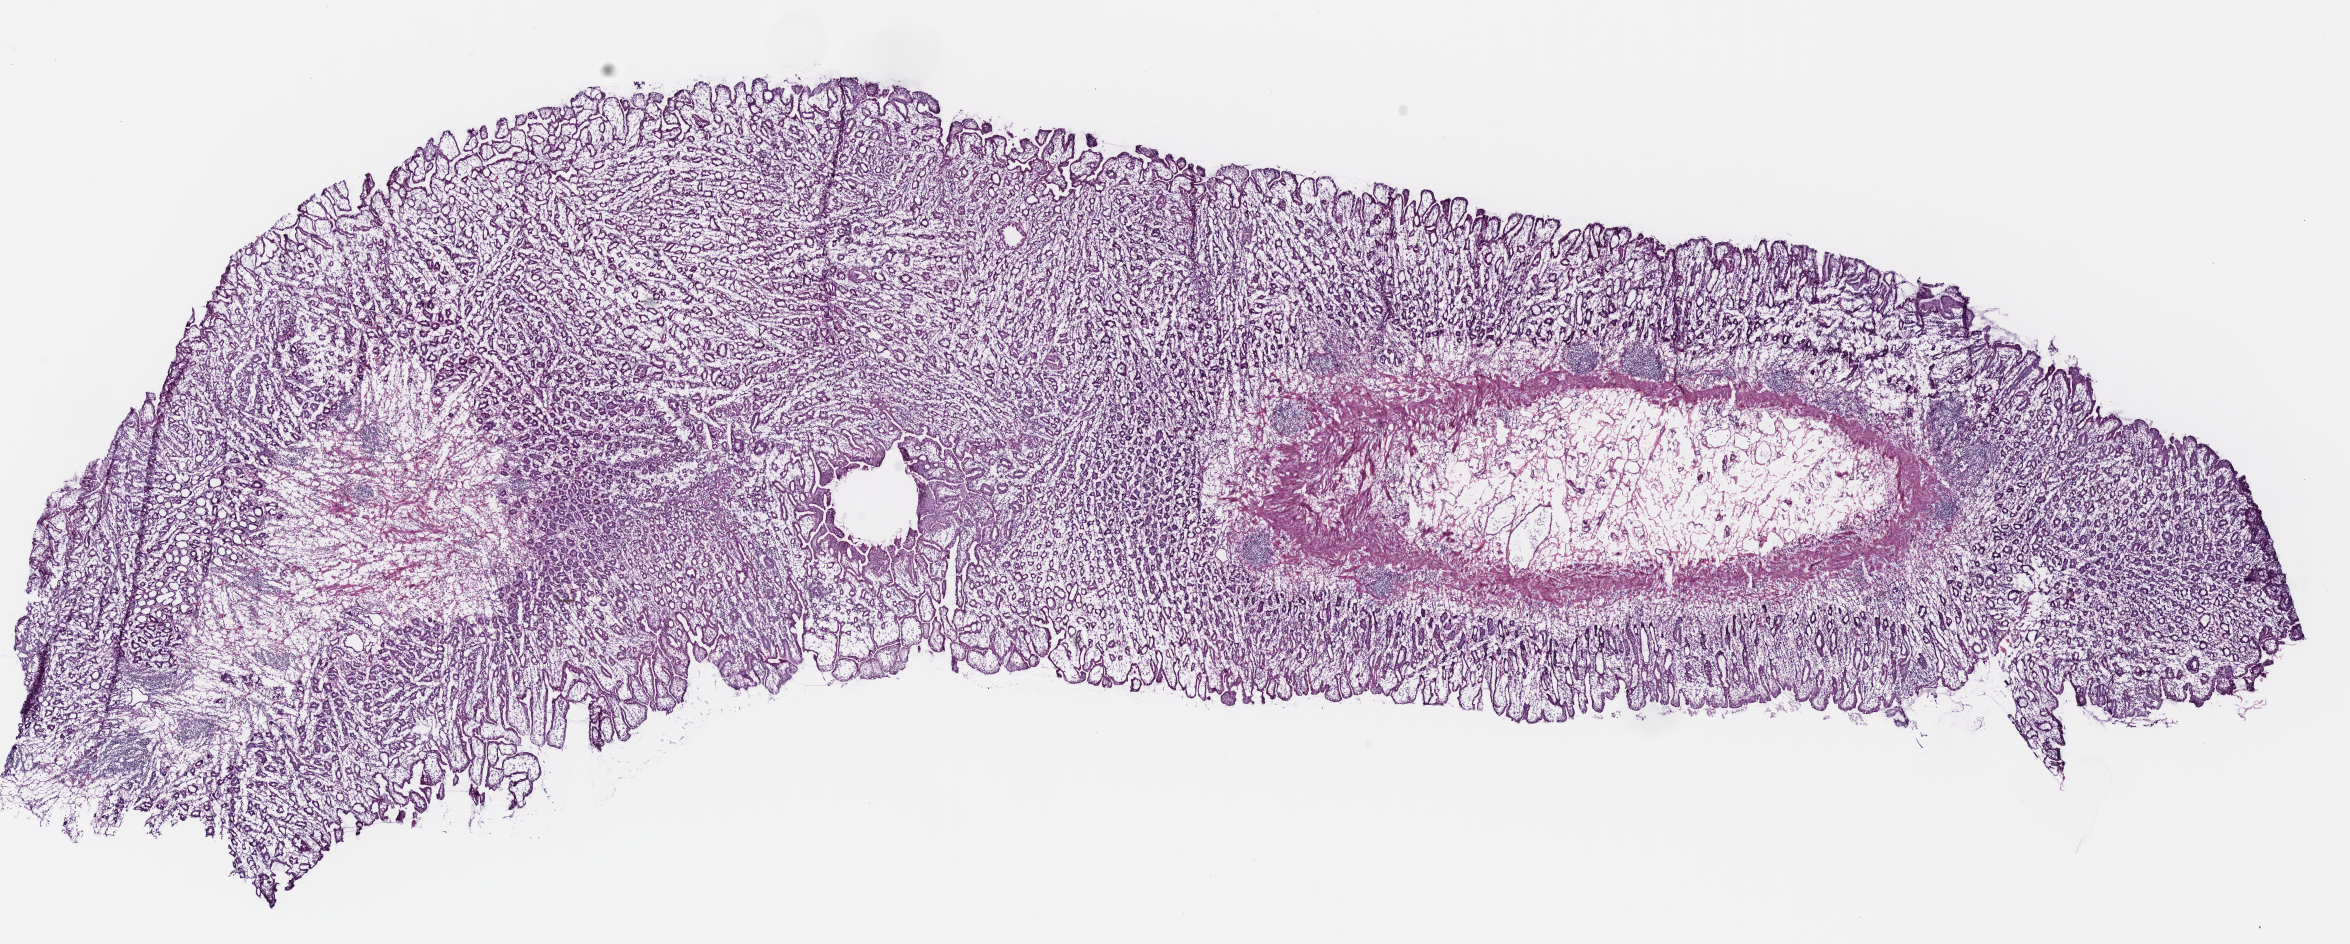
H&E whole-slide image — a low-resolution overview of the entire scanned area, about 18.5 x 7.4 mm (acquisition: 40x scan). Frozen section. Stomach, solid tissue normal (non-tumour tissue) sample. Patient: male, age at initial diagnosis 74 years.
This section: solid tissue normal (non-tumour) sample from the same patient. Patient diagnosis: Adenocarcinoma, intestinal type.